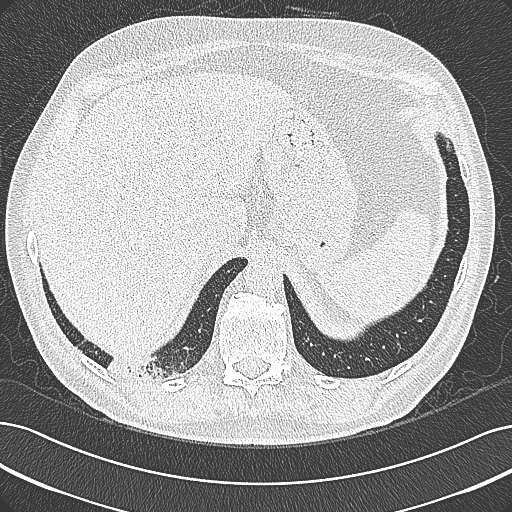
Low-dose screening chest CT, axial slice; baseline screening round; lung window (W 1500 / L -600 HU); 1 mm slice thickness; lung (sharp) reconstruction kernel (B80f); 120 kVp; slice 262 of 355 in the series; 512 × 512 image matrix. Male participant, aged 68 years at enrolment. Former smoker at enrolment.
• Expert-annotated lung lesion, bounding box (x1, y1, x2, y2) in pixels: (93, 336, 197, 396).
• No non-calcified nodule or mass ≥4 mm was recorded by the screening reader at this exam.
• Participant outcome: lung cancer diagnosed 154 days after this screen — mucinous adenocarcinoma, right lower lobe, well differentiated (G1), stage IB (AJCC 6th edition), 50 mm at pathology.